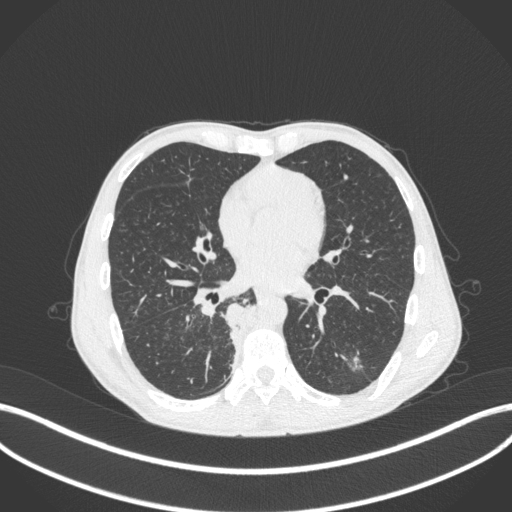
Chest CT, one axial slice; reconstruction kernel B31f; 120 kVp; lung window (W 1500 / L -600 HU); 512 × 512 image matrix. Patient: male, 58 years. Case-level facts recorded for this patient, not image findings: clinical TNM (as recorded): T3 N1 M1.
Annotated regions visible in this slice (rectangle marked by the reading radiologist):
- lung tumour (recorded histology: squamous cell carcinoma): bounding box <225,296,247,356> (left, top, right, bottom; pixels)